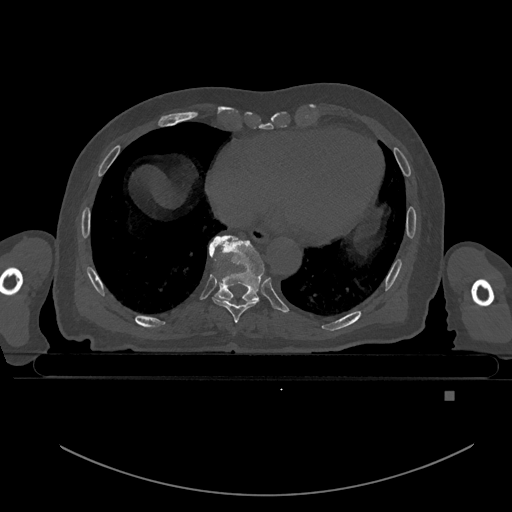
CT including the spine, one axial slice. Slice 176 of 969 in the series (ordered by position). Bone window (W 1800 / L 400 HU). 0.5 mm slice thickness. 512 × 512 image matrix. Male patient, age 82 years. From the clinical record (not read from this slice): primary cancer: prostate; vertebrae with lytic lesions (as recorded): T11, T9, T8, T2.
Annotated regions visible in this slice (semi-automatically segmented with operator editing):
- T8 vertebra: bounding box [x1, y1, x2, y2] px = [212, 296, 258, 323]
- T9 vertebra: [208, 235, 264, 303]